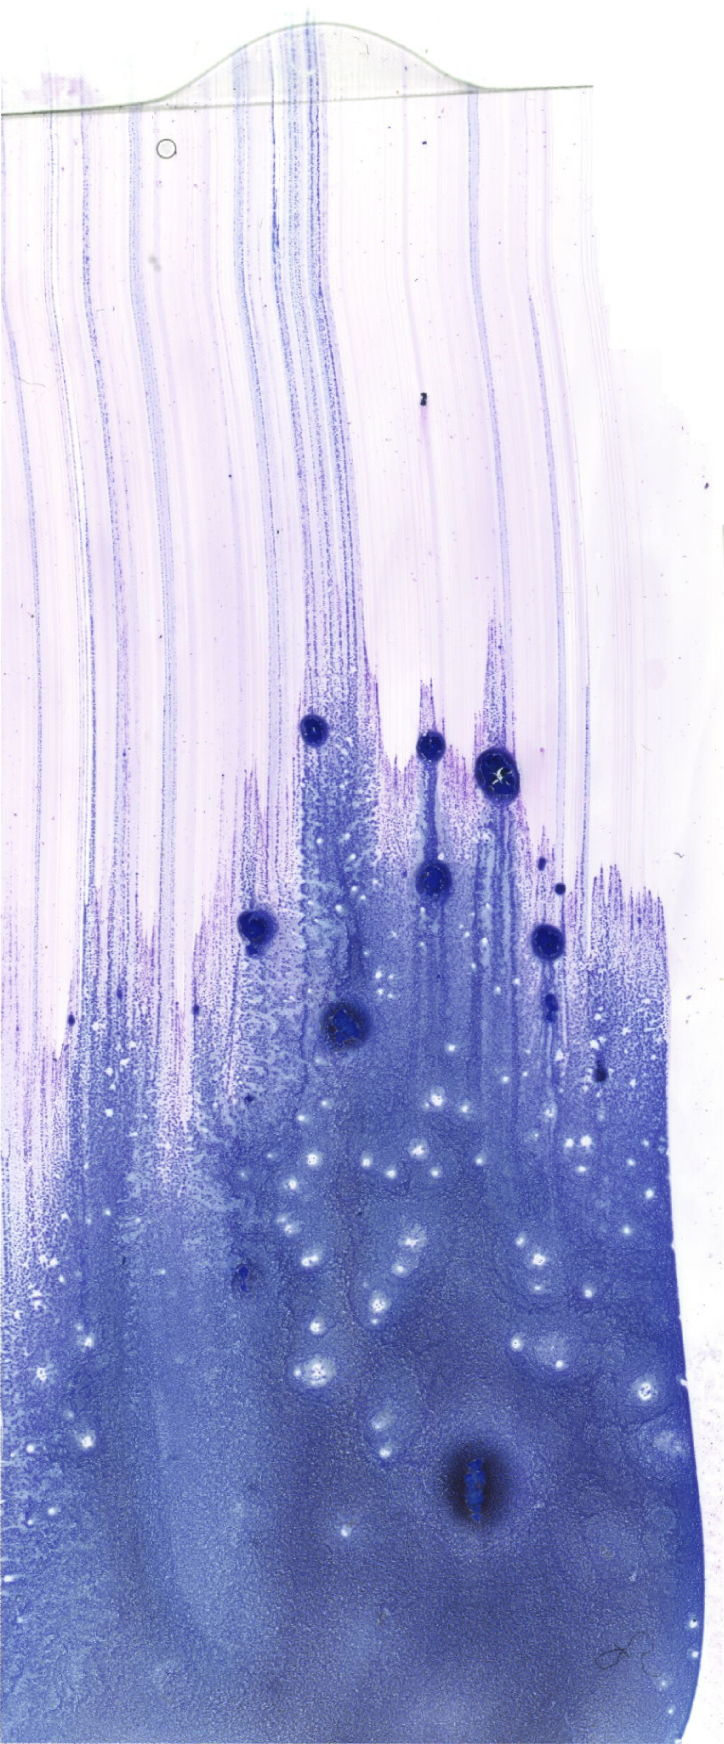
Bone marrow aspirate smear, May-Grünwald-Giemsa (MGG) stain, whole-slide image, a low-resolution overview of the entire scanned area, about 20.5 x 49.4 mm. Female patient.
• diagnosis: Acute Myeloid Leukemia without Maturation